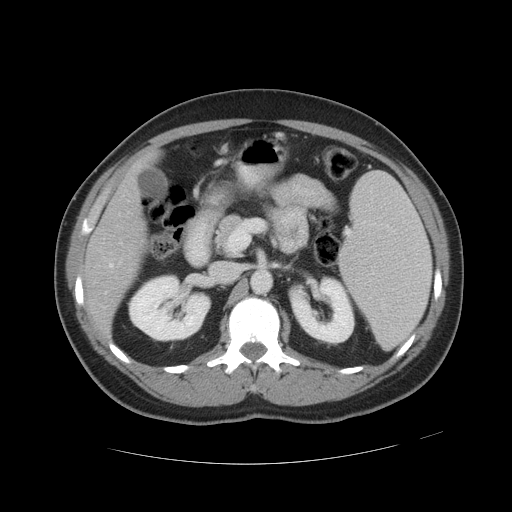
Contrast-enhanced abdominal CT, one axial slice. Slice 25 of 49 in the series (ordered by position). Soft-tissue window (W 400 / L 40 HU). 5 mm slice thickness. 512 × 512 image matrix, field of view 422 × 422 mm. Male patient, age 42 years. From the clinical record (not read from this slice): diagnosis: colorectal cancer liver metastases, imaged before liver resection; multiple liver metastases: yes; largest metastasis: 2.8 cm; disease in both lobes: yes.
Outlined on this slice (outlined manually by an expert reader):
- hepatic veins: bounding box (x1, y1, x2, y2) in pixels: (106, 200, 129, 293)
- liver: (86, 171, 144, 331)
- planned liver remnant (the part of the liver to remain after resection): (86, 234, 141, 331)
- portal vein (with intrahepatic branches): (119, 261, 121, 264)